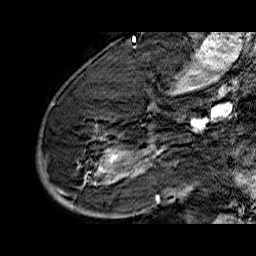
Breast MRI (dynamic contrast-enhanced), one sagittal slice. Dynamic contrast-enhanced series, time point 2 of 6 at this slice position (early post-contrast). 1.5 T. TE 6.5 ms, TR 32.9 ms. 4 mm slice thickness. 256 × 256 image matrix, field of view 200 × 200 mm. Female patient. From the clinical record (not read from this slice): setting: breast cancer imaged before/during neoadjuvant chemotherapy; receptor status: HR-positive, HER2-negative.
Structures marked on this image (semi-automatic segmentation, software-assisted and operator-edited):
- analysis volume of interest (the breast-tissue region the enhancement analysis was run in; not a lesion): bounding box <37,74,176,210> (left, top, right, bottom; pixels)
- tumour enhancement mask (voxels above the 100 % enhancement threshold inside the analysis volume of interest): <50,103,163,202>